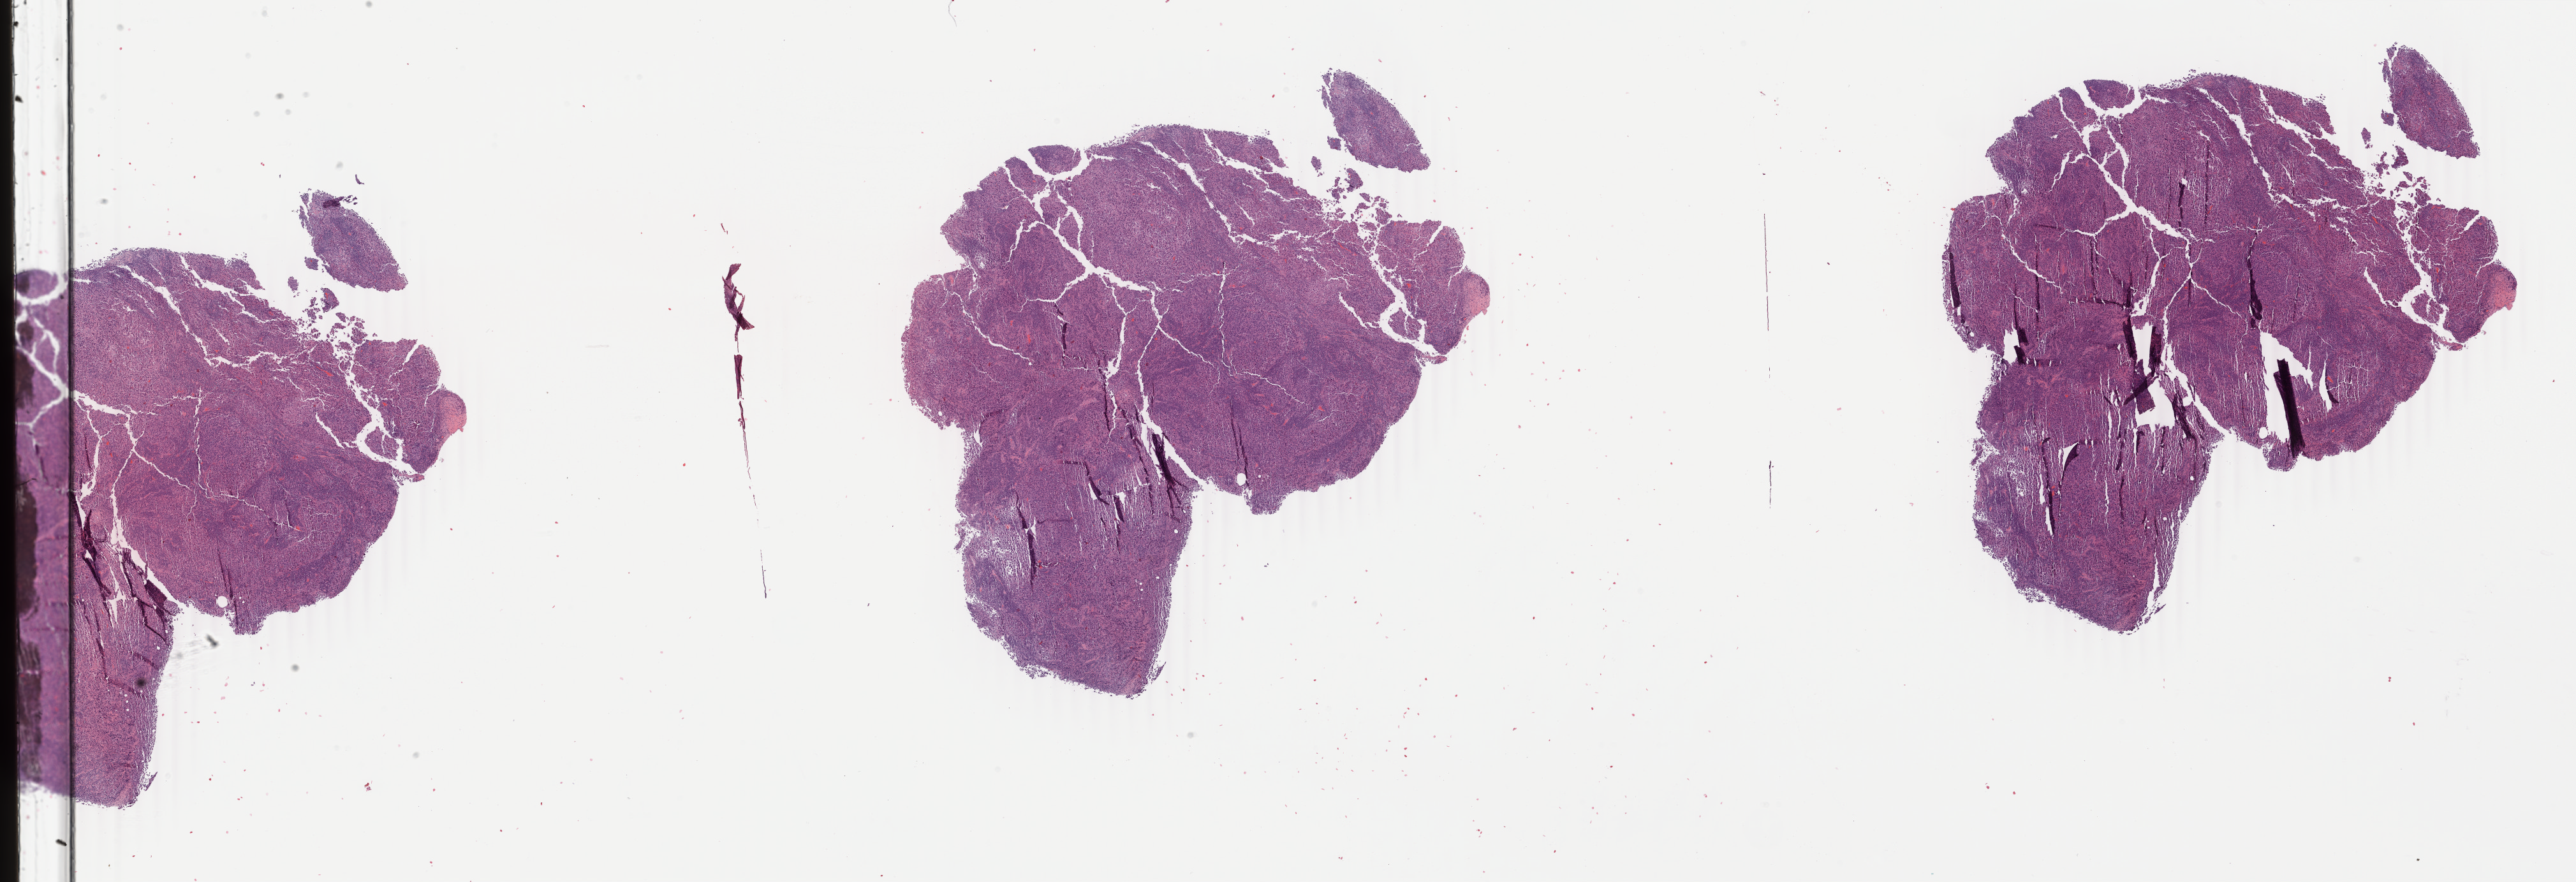
Whole-slide histology image, H&E, shown as a low-resolution overview of the whole scanned area (about 32.1 x 11.0 mm). Formalin-fixed paraffin-embedded (FFPE) diagnostic section. Primary tumour sample from the skin. Female, age 74 years at initial diagnosis.
AJCC pathologic stage: IIIC. Diagnosis: Malignant melanoma, NOS.